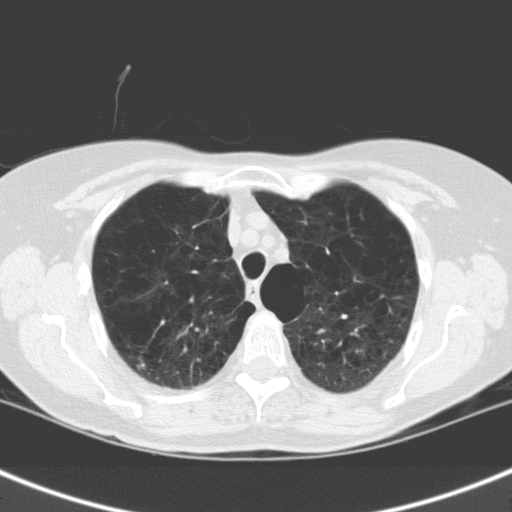
Low-dose screening chest CT, one axial slice. Slice 121 of 158 in the series (ordered by position). Lung window (W 1500 / L -600 HU). 3.2 mm slice thickness. 512 × 512 image matrix, field of view 301 × 301 mm.
Annotated regions visible in this slice (expert manual segmentation):
- lesion 1 (tumor, upper lobe of right lung): bounding box [x1, y1, x2, y2] px = [138, 363, 145, 369]